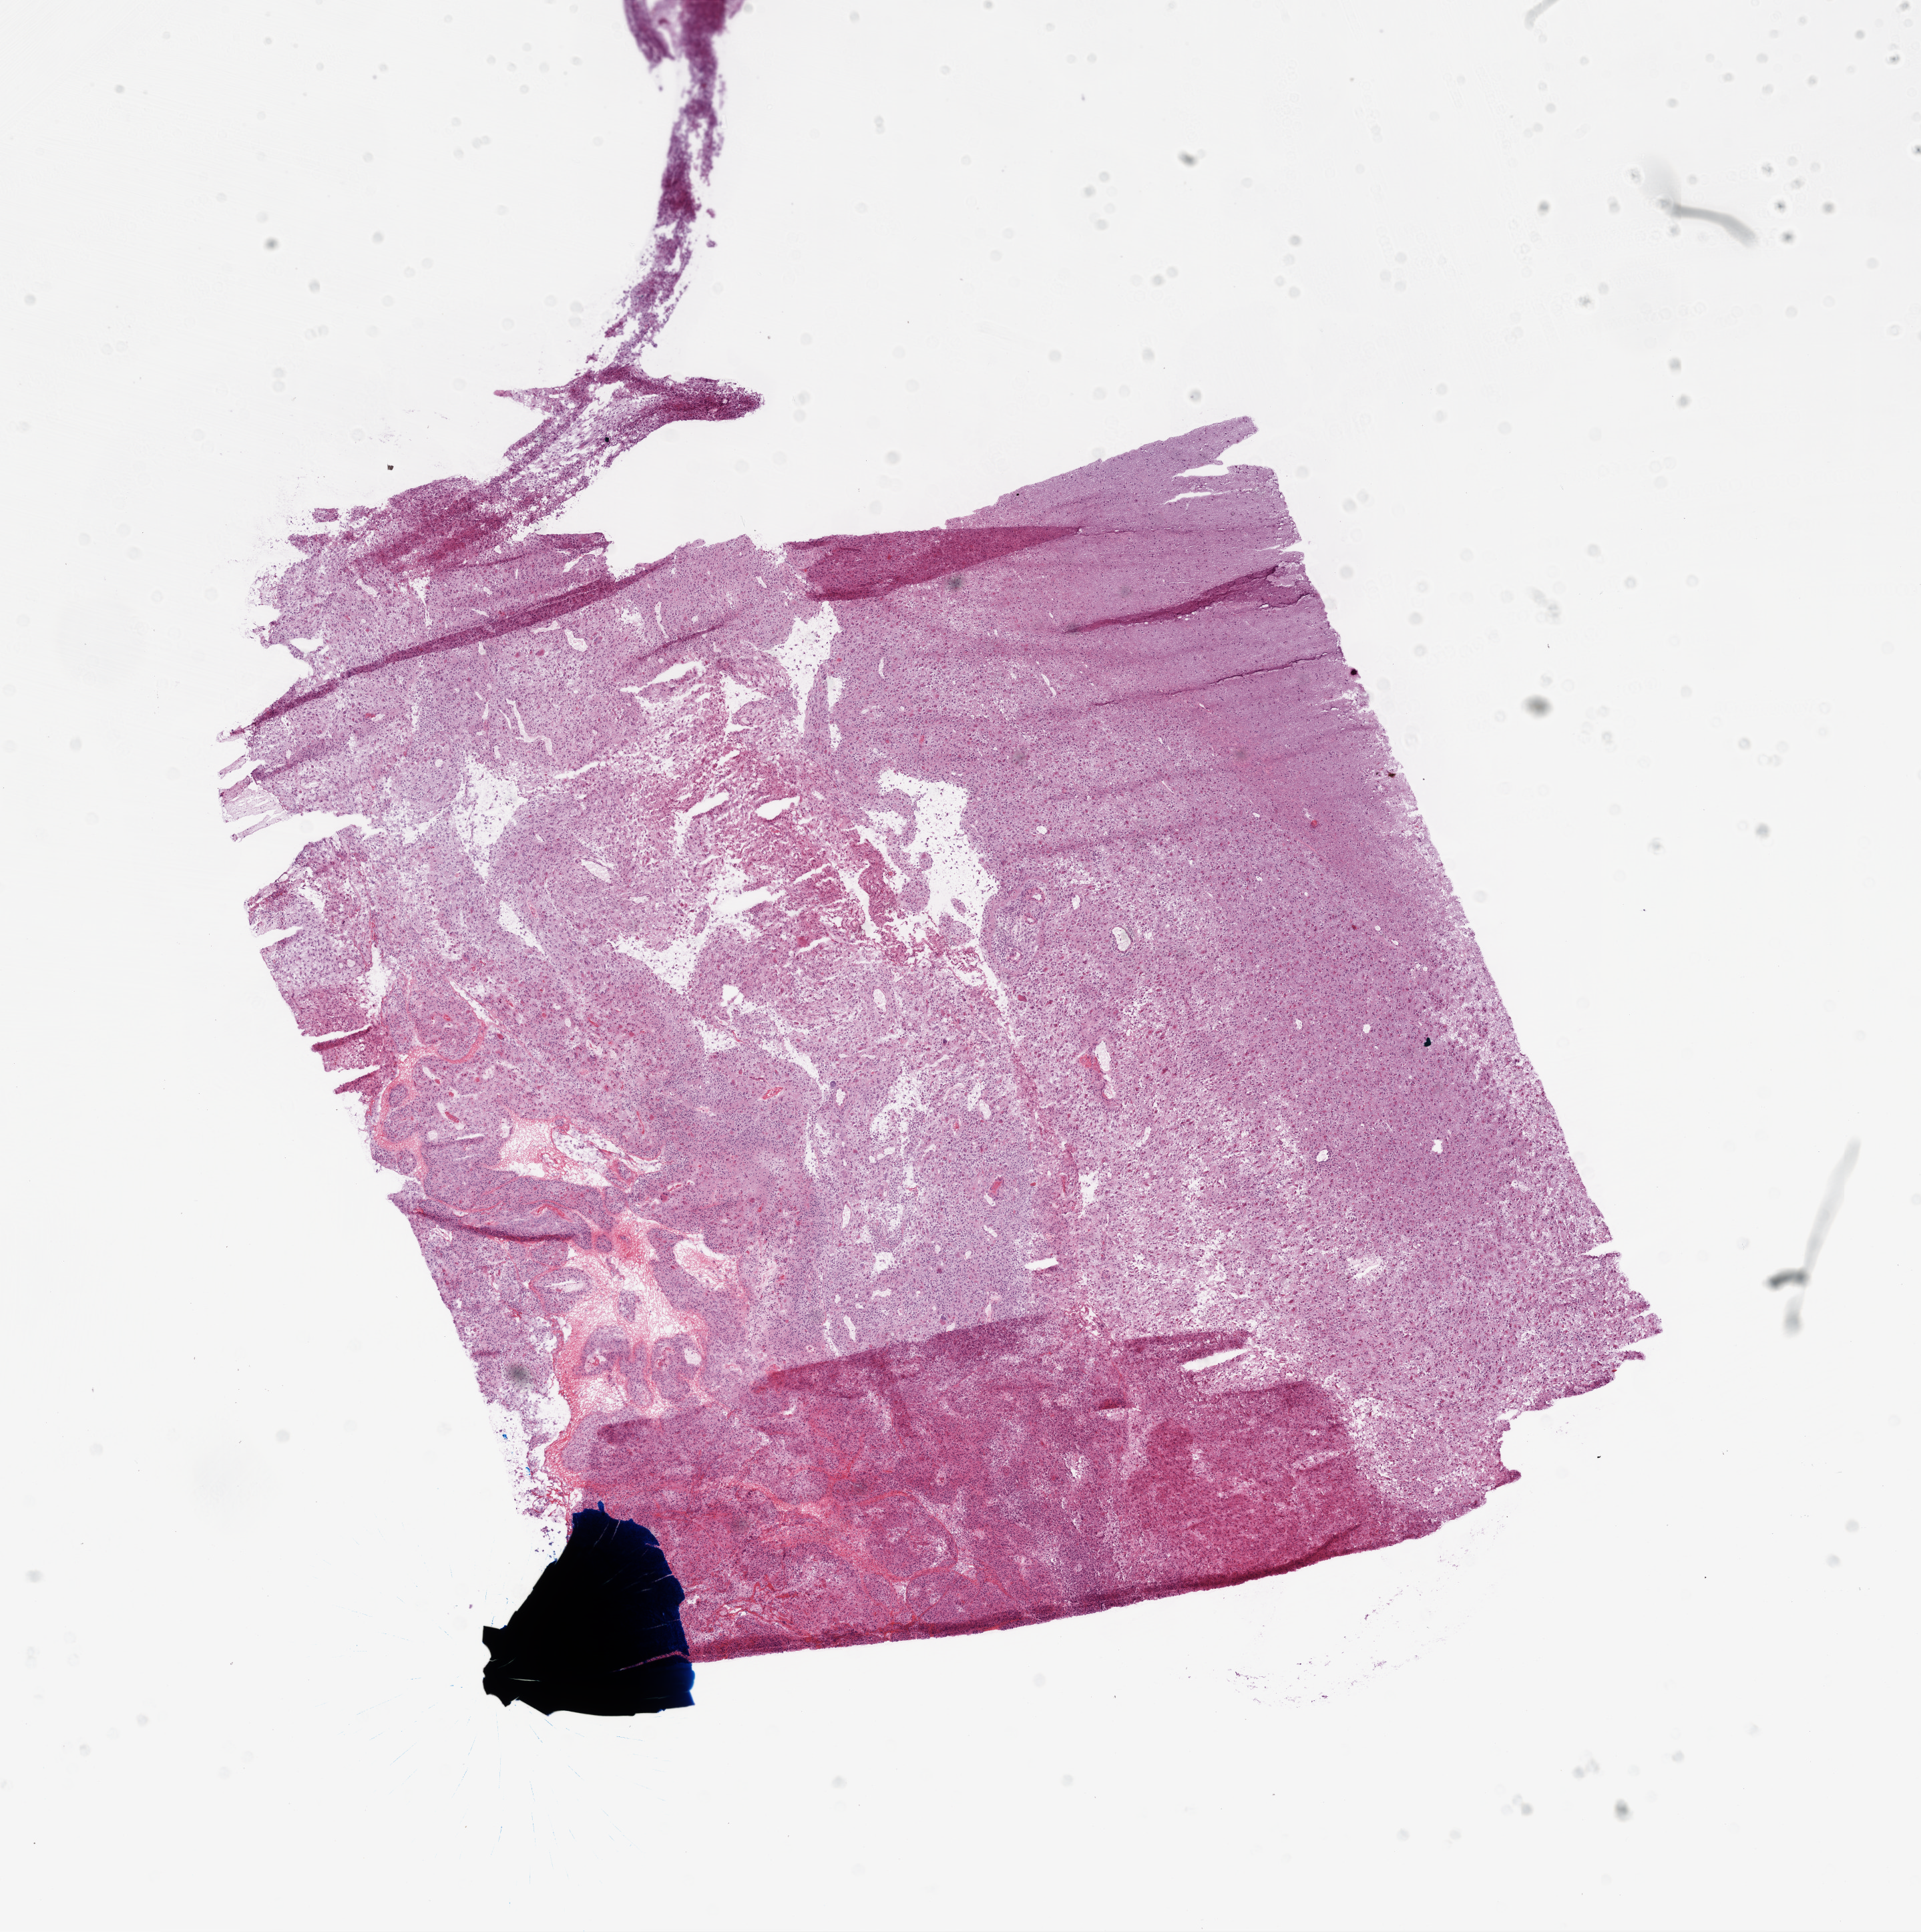
H&E-stained whole-slide image, shown as a low-resolution overview of the whole scanned area (about 11.6 x 11.7 mm, from a 20x scan), frozen section, primary tumour sample from the brain. Female, age 79 years at initial diagnosis. Slide review estimates, as recorded: tumour cells 75%, tumour nuclei 80%, normal cells 20%, stromal cells 0%, necrosis 5%.
Pathologic diagnosis: Glioblastoma.